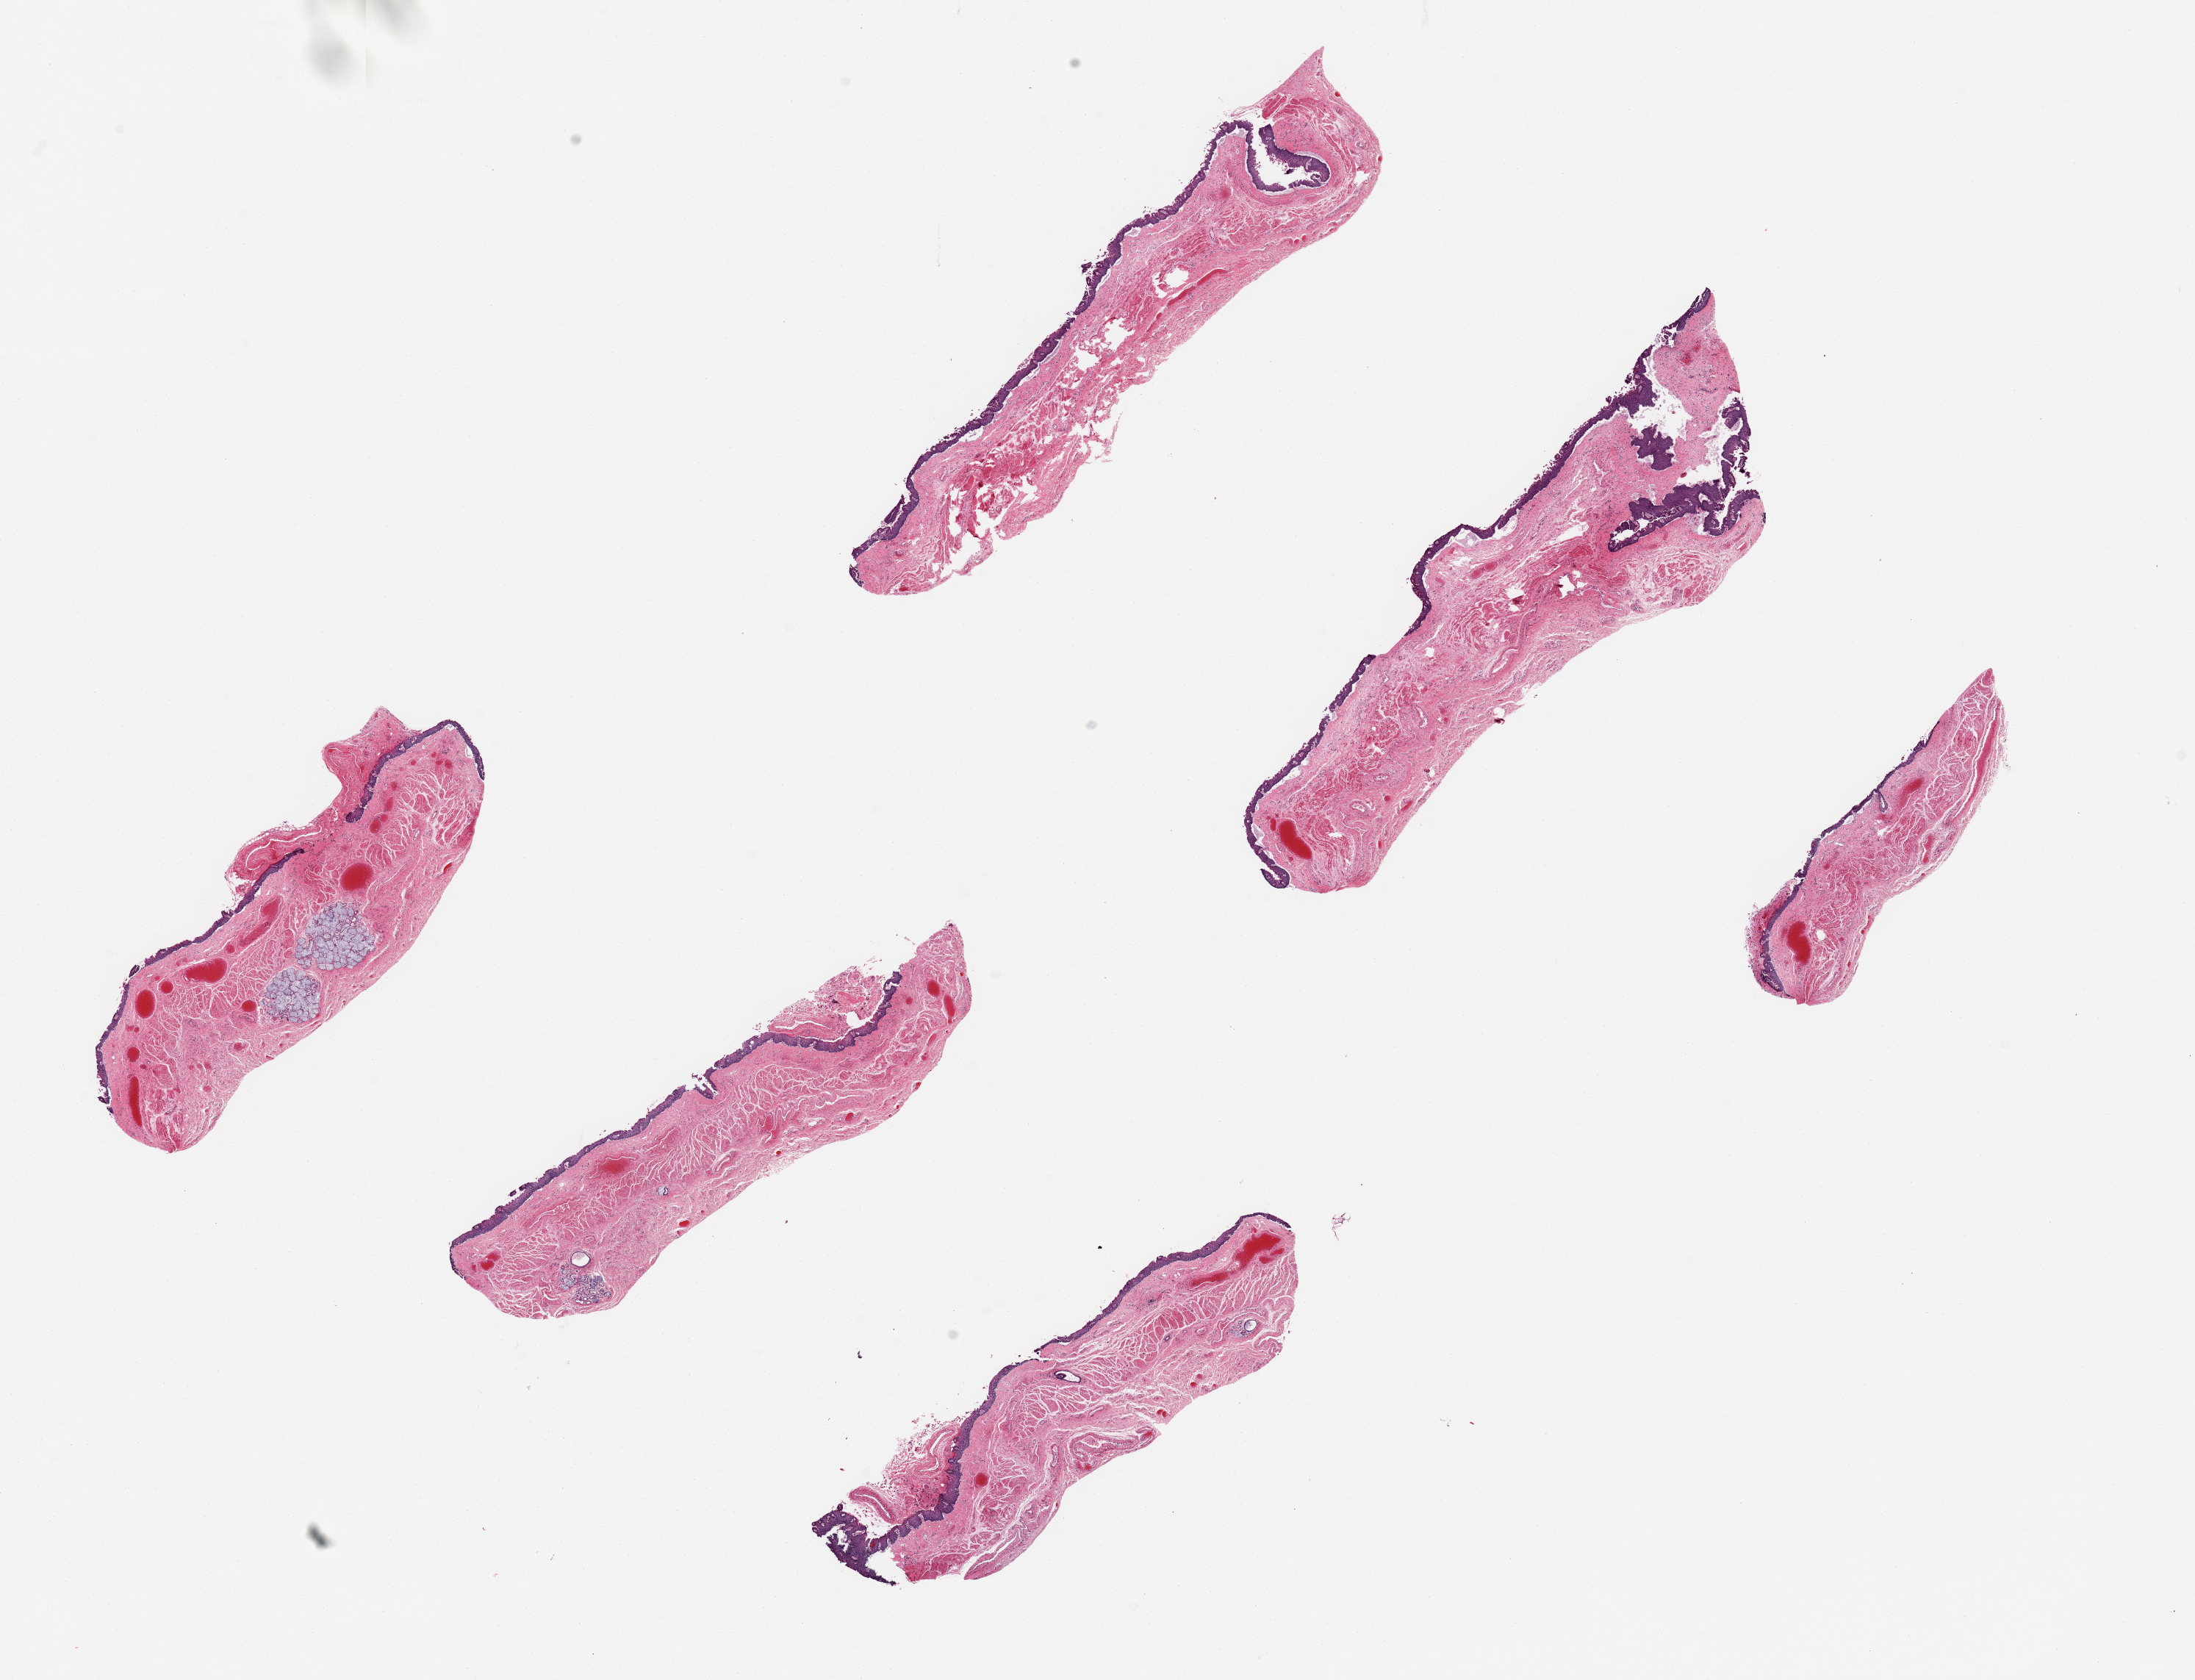
Whole-slide image, haematoxylin and eosin stain — whole scanned area (about 23.6 x 18.1 mm) shown as a low-resolution overview, PAXgene-fixed, paraffin-embedded tissue, target tissue: esophageal mucous membrane, donor tissue sample. Donor: female.
• pathologist's review note for this sample: 6 pieces up to 7x2 mm; squamous surface partly sloughed and detached; dilated submucosal veins (varices)